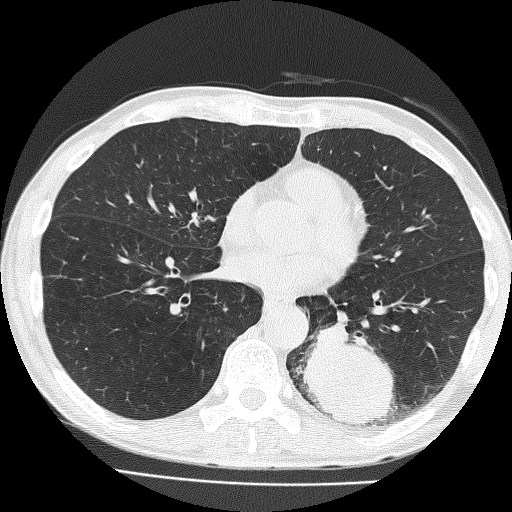
Low-dose screening chest CT, one axial slice; position 72 of 160 along the scan axis; reconstruction kernel FC51; 120 kVp; lung window (W 1500 / L -600 HU); 512 × 512 image matrix, field of view 324 × 324 mm.
Structures marked on this image (manually delineated by an expert):
- lesion 1 (tumor, lower lobe of left lung): box from (x=301, y=323) to (x=396, y=425) px